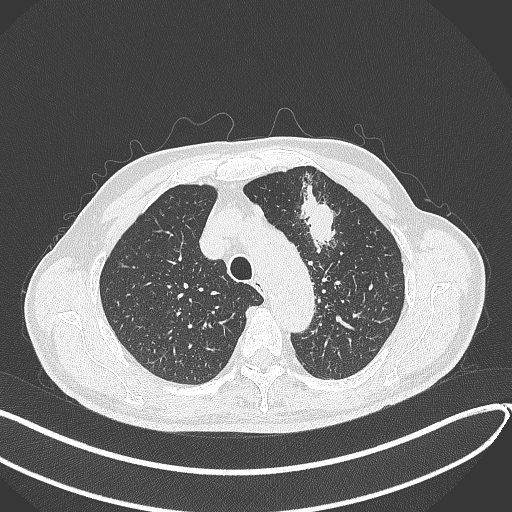
Chest CT, one axial slice. Position 323 of 459 along the scan axis. 120 kVp. Lung window (W 1500 / L -600 HU). 512 × 512 image matrix. Male patient, age 74 years. Case-level facts recorded for this patient, not image findings: clinical TNM (as recorded): T2b N0 M1c.
Annotated regions visible in this slice (rectangle marked by the reading radiologist):
- lung tumour (recorded histology: adenocarcinoma): box from (x=298, y=182) to (x=344, y=257) px